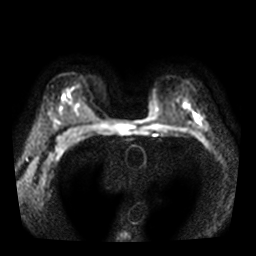
Breast MRI, one axial slice; slice 24 of 36 in the series (ordered by position); diffusion-weighted series; image 2 of 4 stored at this slice position (different b-values; order by instance number); 3 T; 256 × 256 image matrix. Female patient.
Structures marked on this image (expert manual segmentation):
- tumour on diffusion-weighted imaging: box from (x=195, y=115) to (x=199, y=122) px